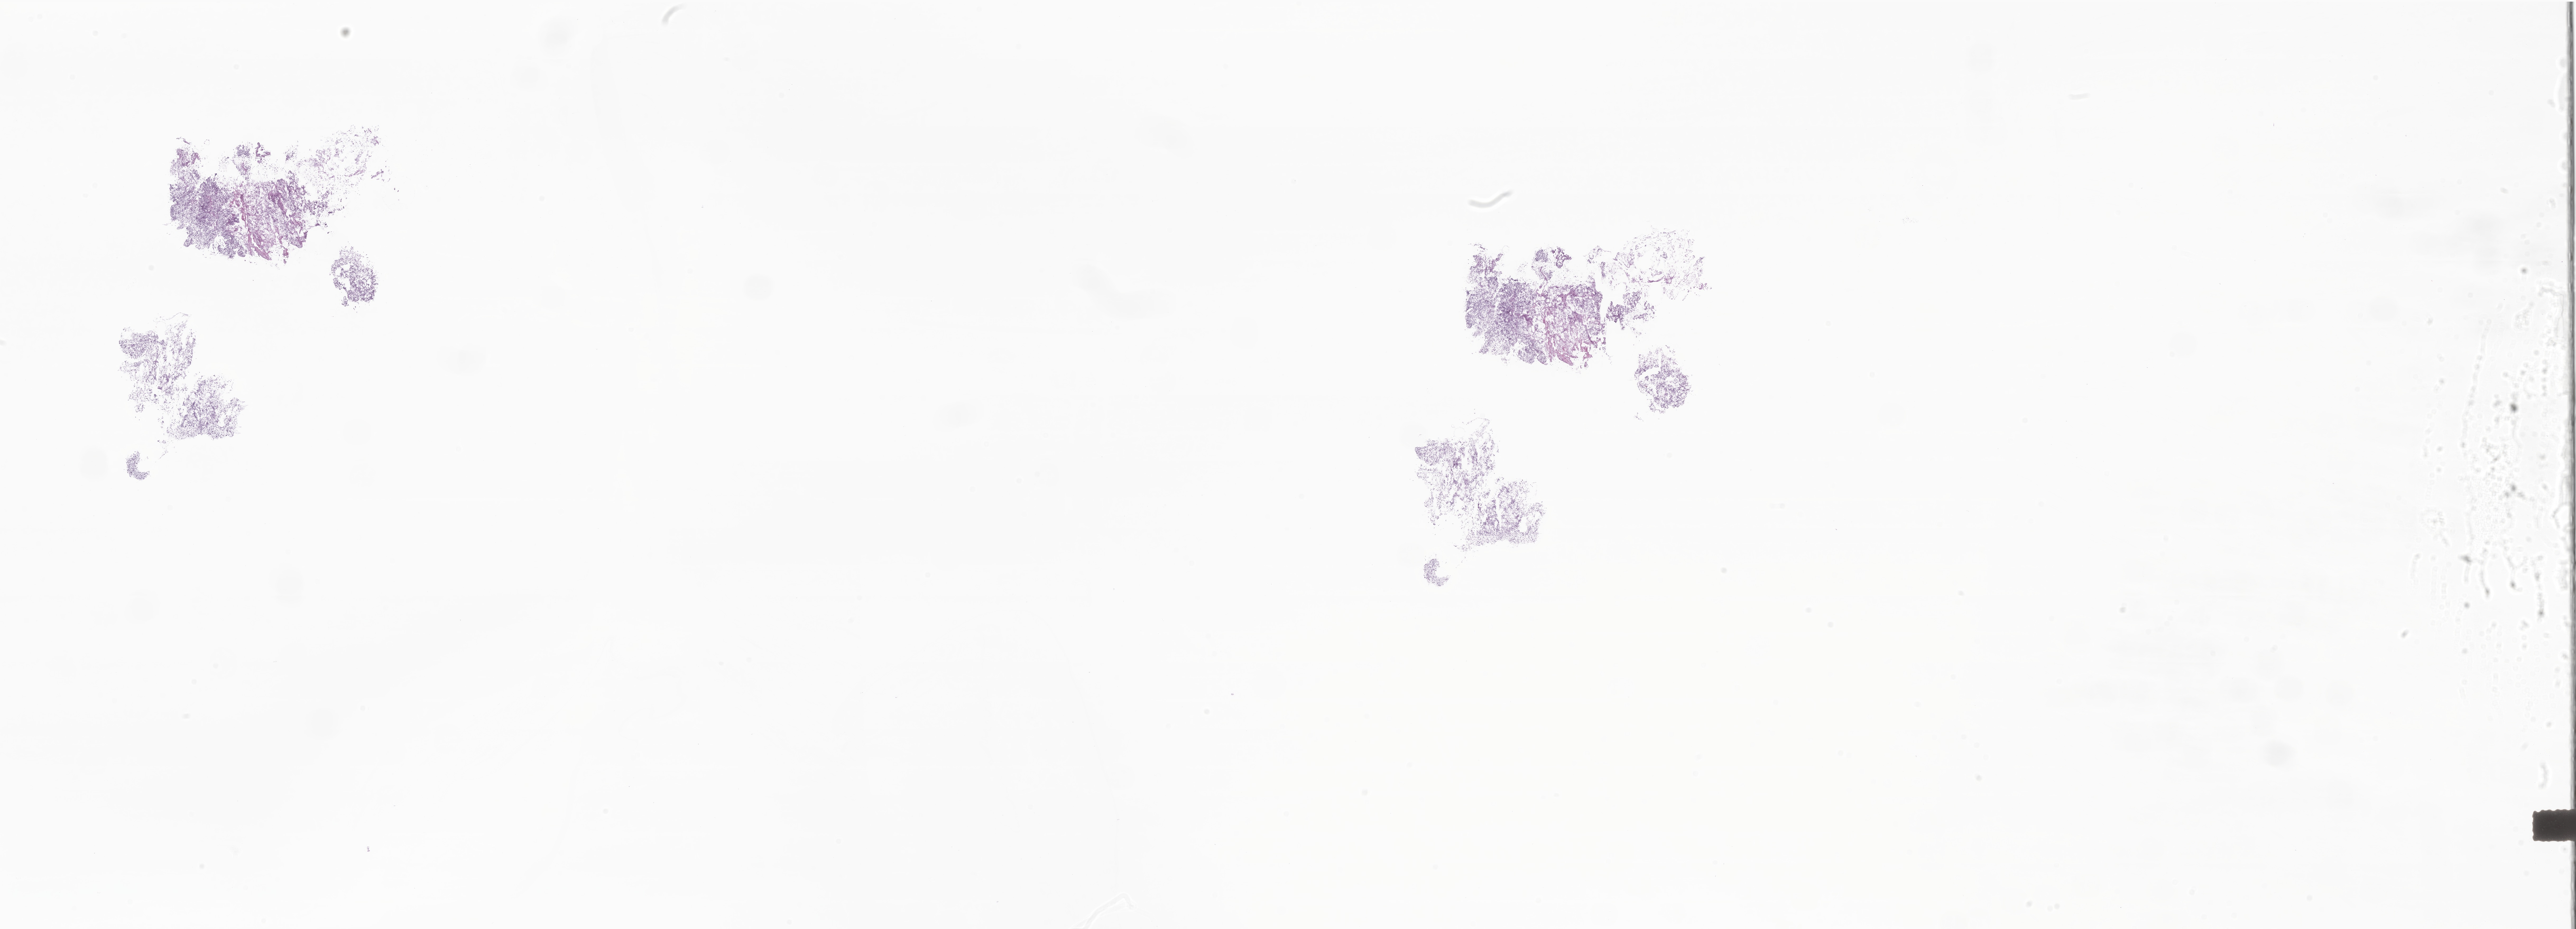
Whole-slide image, H&E stain of tumor tissue from the head and neck, low-resolution overview of the scanned area, about 41.1 x 14.8 mm; frozen section. Patient female; age 62 months (5 years 2 months).
Diagnosis: Rhabdomyosarcoma, NOS.